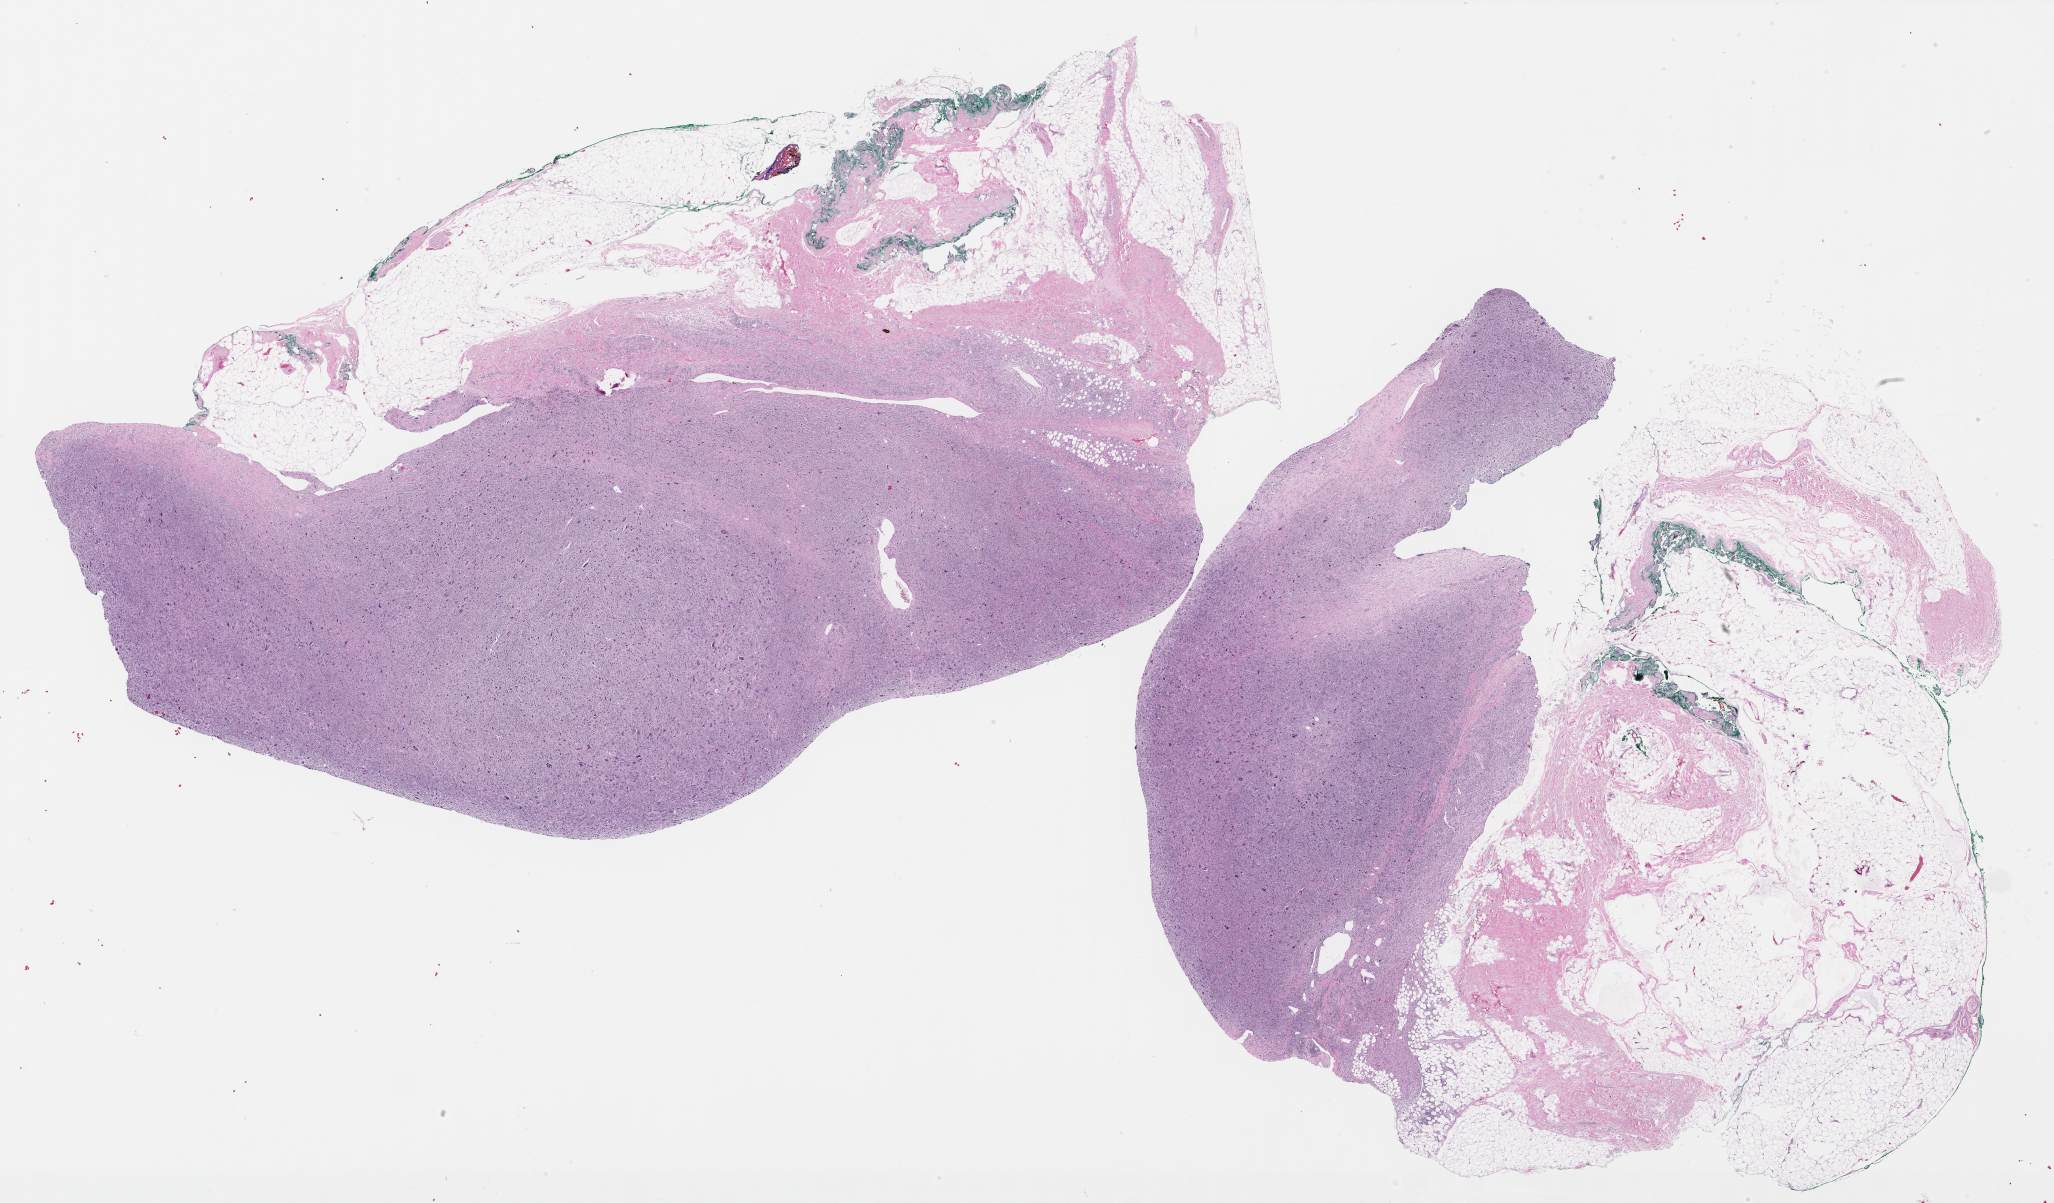
Hematoxylin and eosin (H&E) stained whole-slide image — shown as a low-resolution overview of the whole scanned area (about 33.0 x 19.3 mm); formalin-fixed paraffin-embedded (FFPE) diagnostic section; primary tumour sample from the connective, subcutaneous and other soft tissues. Male, age 71 years at initial diagnosis.
Diagnosis: Undifferentiated sarcoma (connective, subcutaneous and other soft tissues of trunk, NOS).